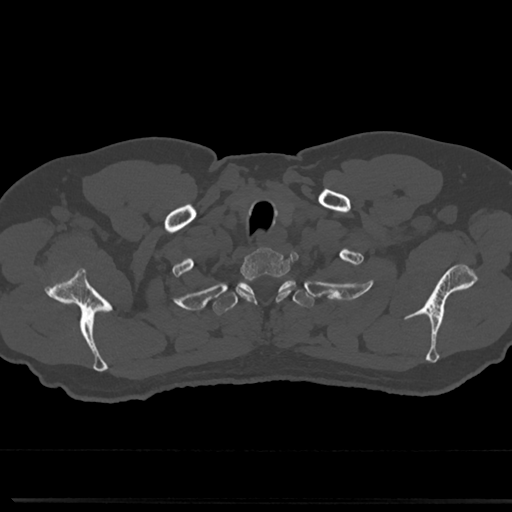
CT including the spine, one axial slice; slice 655 of 817 in the series (ordered by position); 120 kVp; bone window (W 1800 / L 400 HU); 0.5 mm slice thickness; 512 × 512 image matrix, field of view 355 × 355 mm. Patient: male, 61 years. From the clinical record (not read from this slice): primary cancer: prostate.
Outlined on this slice (semi-automatically segmented with operator editing):
- T1 vertebra: bounding box <239,249,288,277> (left, top, right, bottom; pixels)
- T2 vertebra: <219,275,310,312>